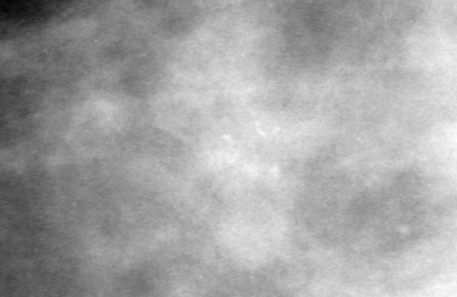
Crop from a digitized film mammogram around one marked abnormality, left breast, CC view.
- Marked abnormality: calcifications, morphology pleomorphic, distribution clustered; BI-RADS assessment category 4; pathology (as recorded): benign.